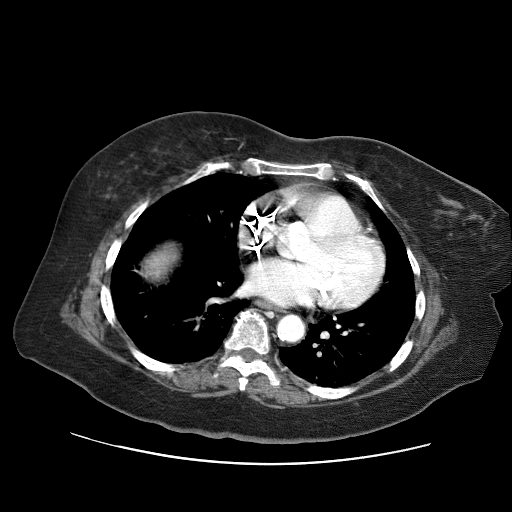
Contrast-enhanced abdominal CT (liver protocol), one axial slice. Position 67 of 71 along the scan axis. 120 kVp. Soft-tissue window (W 400 / L 40 HU). 2.5 mm slice thickness. 512 × 512 image matrix, field of view 400 × 400 mm. From the clinical record (not read from this slice): diagnosis: hepatocellular carcinoma (patient treated with transarterial chemoembolisation; whether this scan precedes or follows treatment is not stated here); TNM stage (as recorded): Stage-II; Child-Pugh class: A; tumour differentiation: poorly differentiated; tumour size: 5 cm.
Structures marked on this image (semi-automatically segmented with operator editing):
- abdominal aorta: bounding box (x1, y1, x2, y2) in pixels: (278, 316, 303, 339)
- liver parenchyma outside the tumour (the mass and vessels are separate outlines, so this box may not span the whole liver): (146, 246, 176, 276)